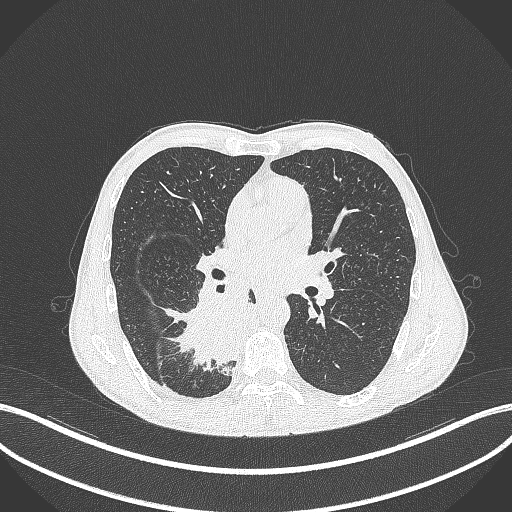
Chest CT, one axial slice; slice 196 of 371 in the series (ordered by position); reconstruction kernel B70f; lung window (W 1500 / L -600 HU); 1 mm slice thickness; 512 × 512 image matrix, field of view 400 × 400 mm. Male patient, age 58 years. From the clinical record (not read from this slice): clinical TNM (as recorded): T3 N1 M1.
Structures marked on this image (rectangle marked by the reading radiologist):
- lung tumour (recorded histology: squamous cell carcinoma): box from (x=158, y=281) to (x=257, y=375) px